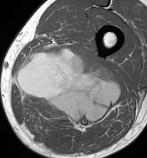
MRI of an extremity soft-tissue mass, one axial slice. Slice 49 of 86 in the series (ordered by position). MR volume resampled by the dataset authors to the PET/CT grid (not the native acquisition matrix). 3.27 mm slice thickness. 147 × 158 image matrix. Male patient. From the clinical record (not read from this slice): histological type: undifferentiated pleomorphic liposarcoma; grade: high; site of the primary tumour: left thigh.
Structures marked on this image (expert contour drawn on MRI and transferred to this co-registered scan by the dataset authors):
- gross tumour volume including surrounding oedema: bounding box <14,44,122,130> (left, top, right, bottom; pixels)
- gross tumour volume (mass): <16,44,122,130>